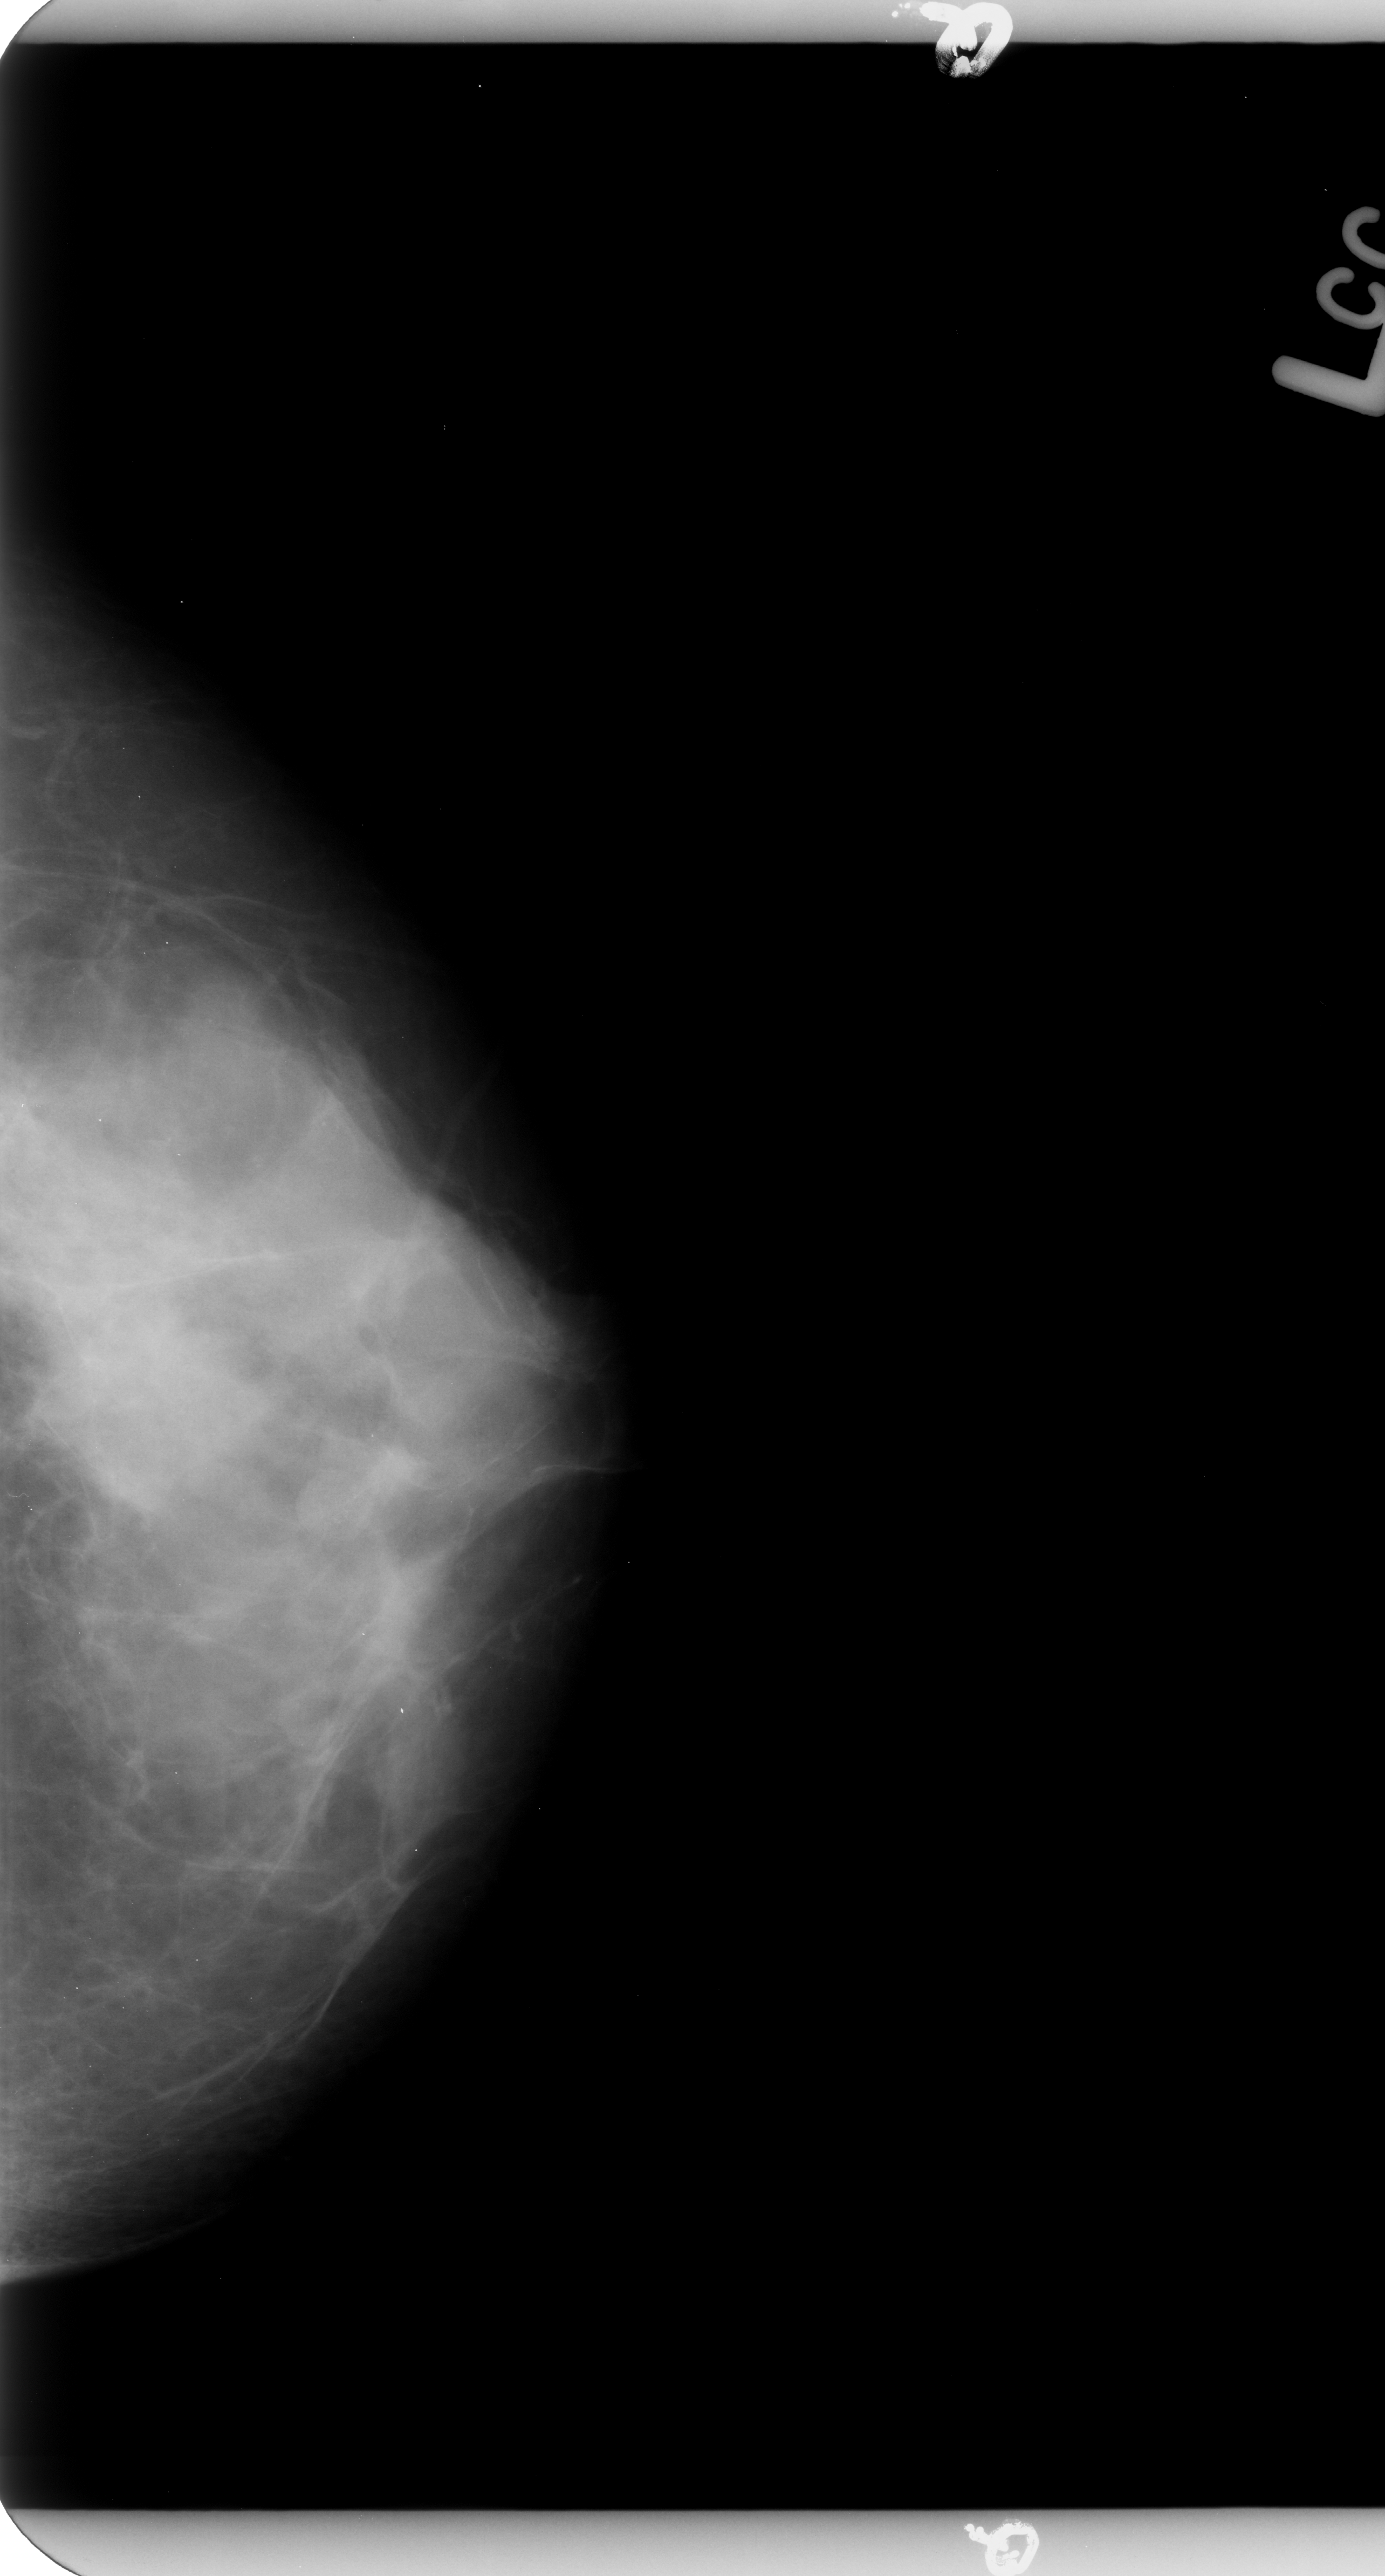
Scanned film-screen mammogram, left breast, CC view, BI-RADS breast density category 4 (scale 1–4).
- Mass, shape round, margins circumscribed; BI-RADS assessment category 3; pathology result (as recorded, not read from the image): benign.